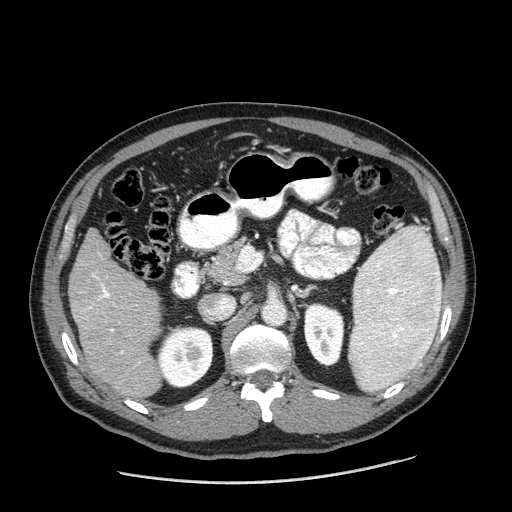
Contrast-enhanced abdominal CT (liver protocol), one axial slice; position 85 of 198 along the scan axis; reconstruction kernel STANDARD; 120 kVp; one of 2 acquisitions stored at this slice position; soft-tissue window (W 400 / L 40 HU); 512 × 512 image matrix, field of view 400 × 400 mm. Case-level facts recorded for this patient, not image findings: diagnosis: hepatocellular carcinoma (patient treated with transarterial chemoembolisation; whether this scan precedes or follows treatment is not stated here); TNM stage (as recorded): Stage-II; Child-Pugh class: A; tumour differentiation: moderately differentiated; tumour nodularity: multinodular.
Structures marked on this image (semi-automatically segmented with operator editing):
- liver parenchyma outside the tumour (the mass and vessels are separate outlines, so this box may not span the whole liver): bounding box (x1, y1, x2, y2) in pixels: (68, 228, 161, 396)
- liver vessels: (86, 275, 123, 354)